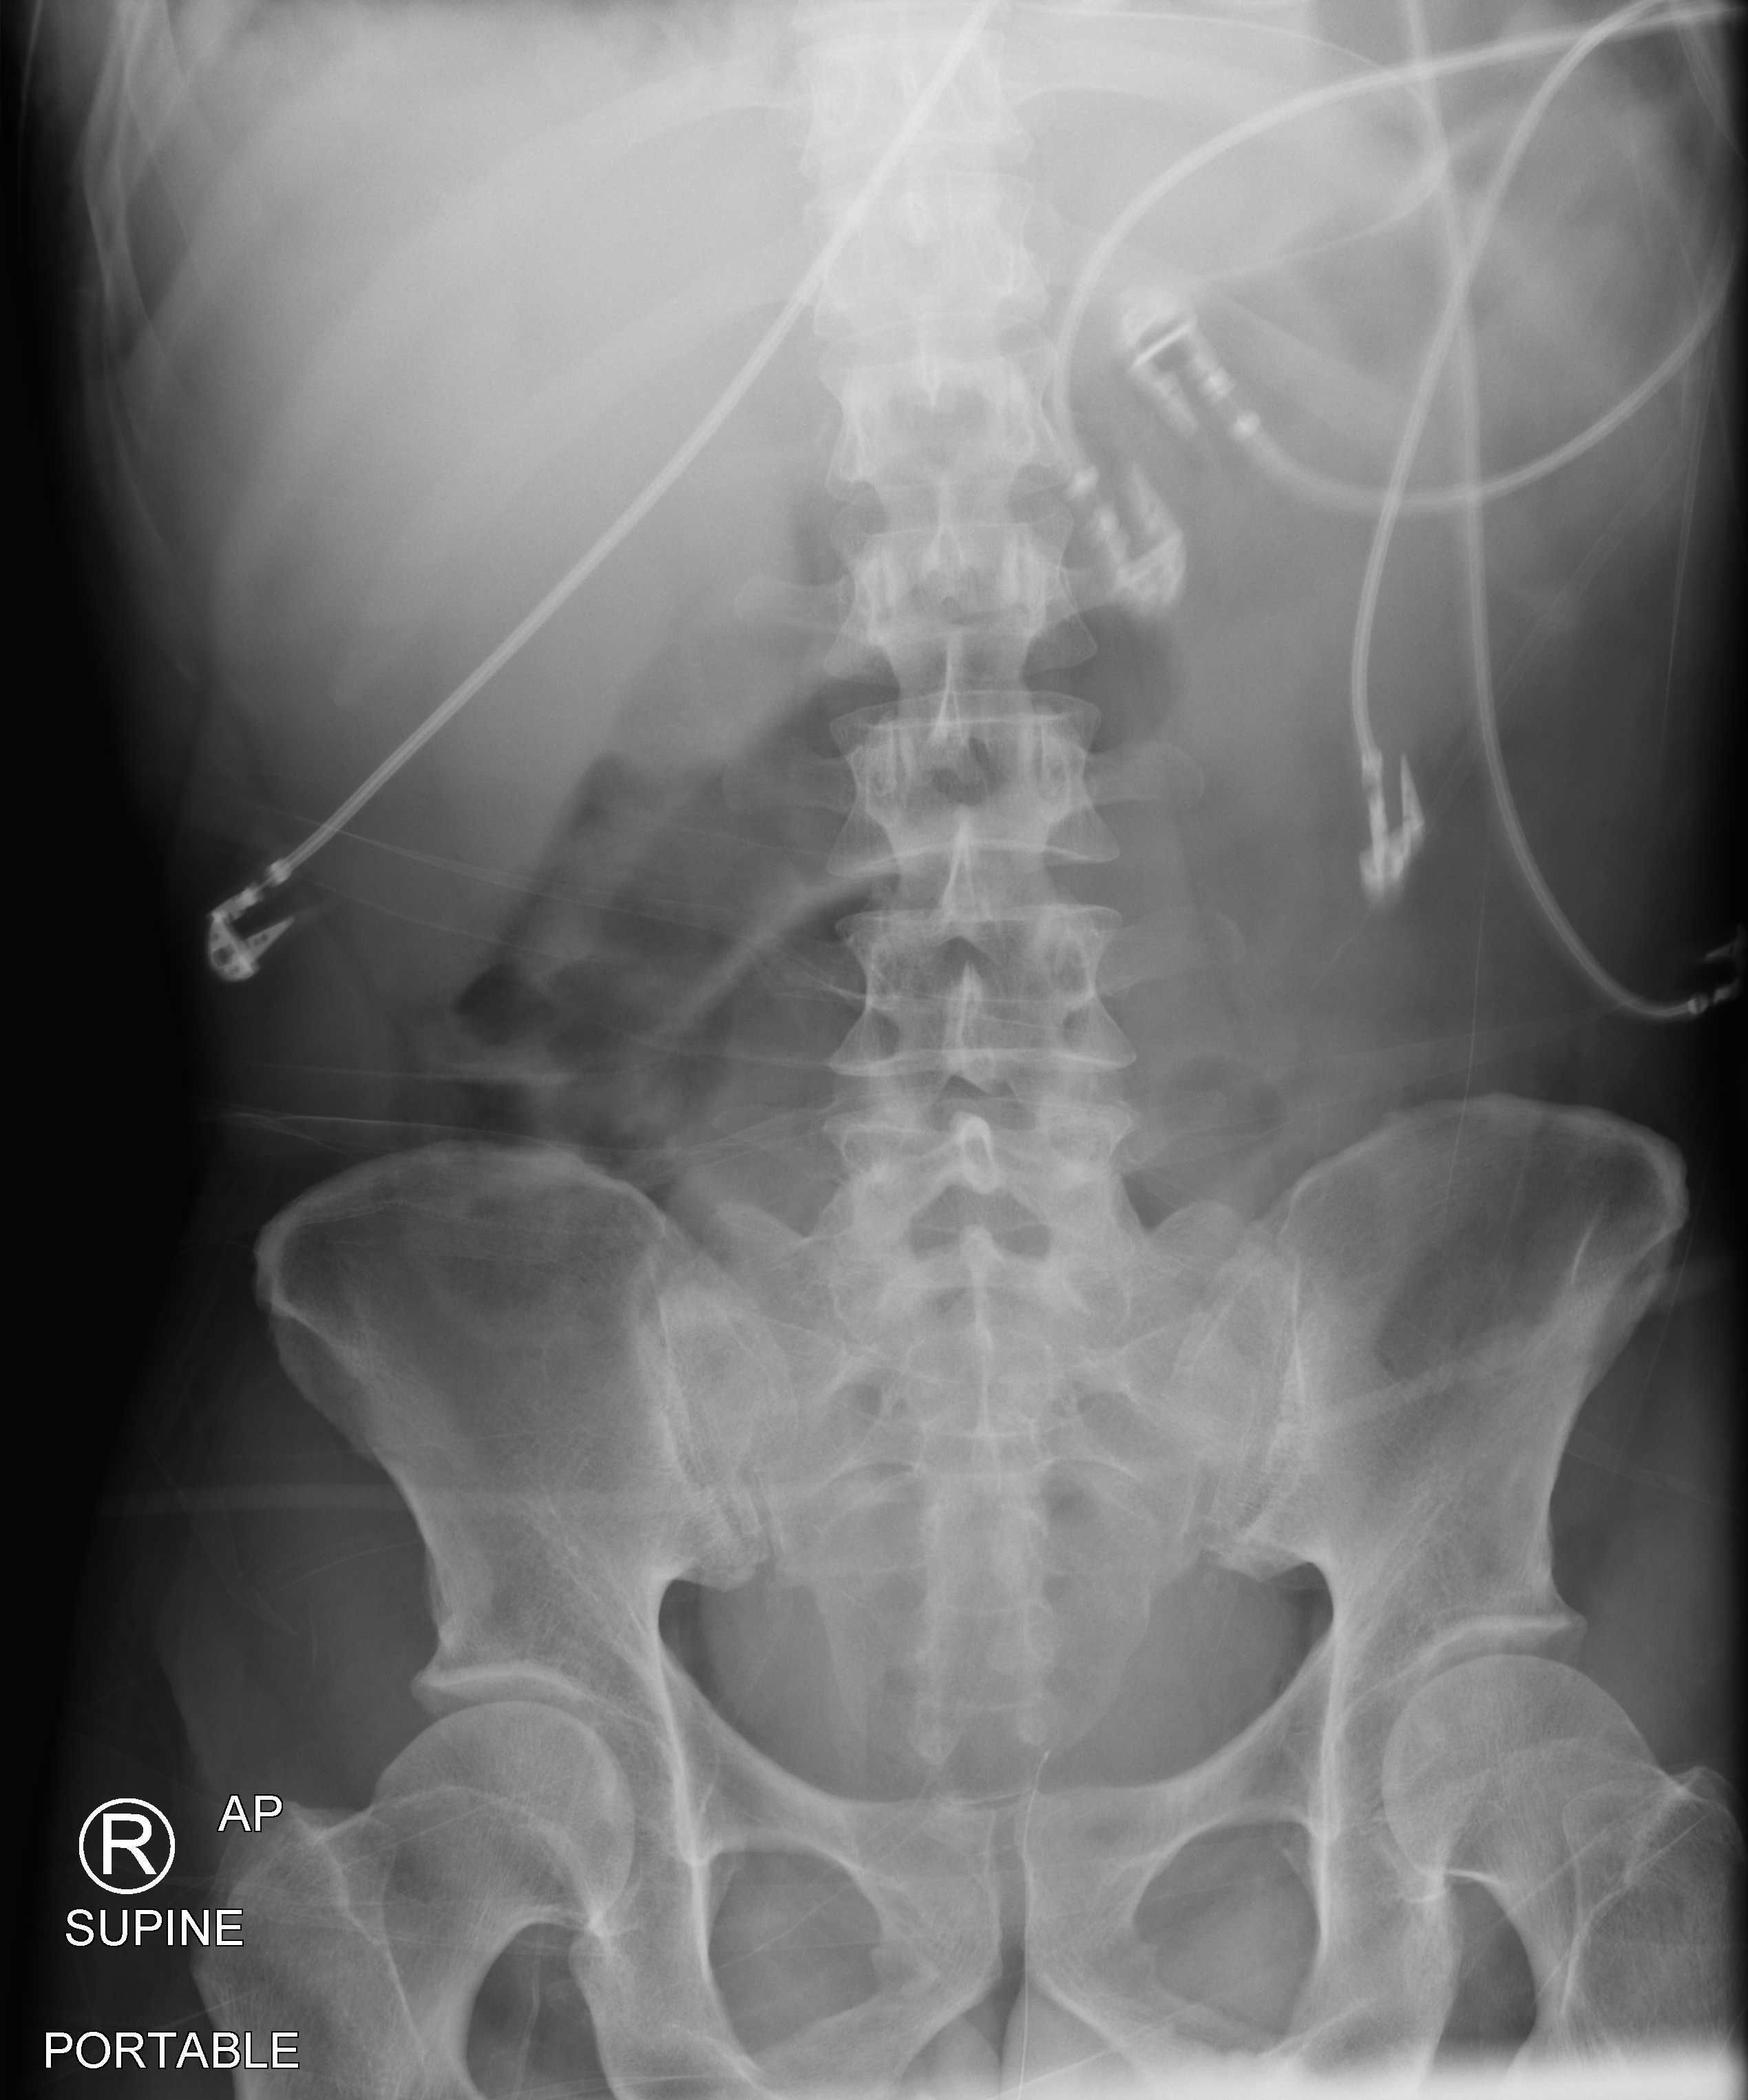
Portable abdomen radiograph; anteroposterior (AP) projection. Patient hospitalised with COVID-19; male, aged 18–59 years.
From the hospital-stay record, not from the radiograph (when in the stay this image was taken is not recorded):
- mechanically ventilated during this hospital stay: yes